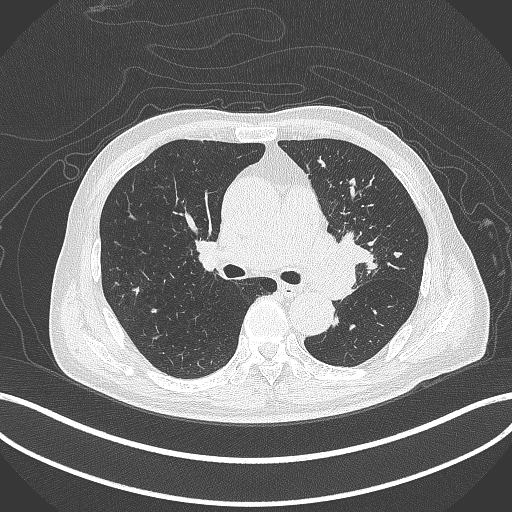
Chest CT, one axial slice; reconstruction kernel B70f; 120 kVp; lung window (W 1500 / L -600 HU); 512 × 512 image matrix. Patient: male, 77 years. From the clinical record (not read from this slice): clinical TNM (as recorded): T3 N1 M0.
Outlined on this slice (bounding box drawn by a radiologist):
- lung tumour (recorded histology: adenocarcinoma): bounding box (x1, y1, x2, y2) in pixels: (305, 226, 369, 300)